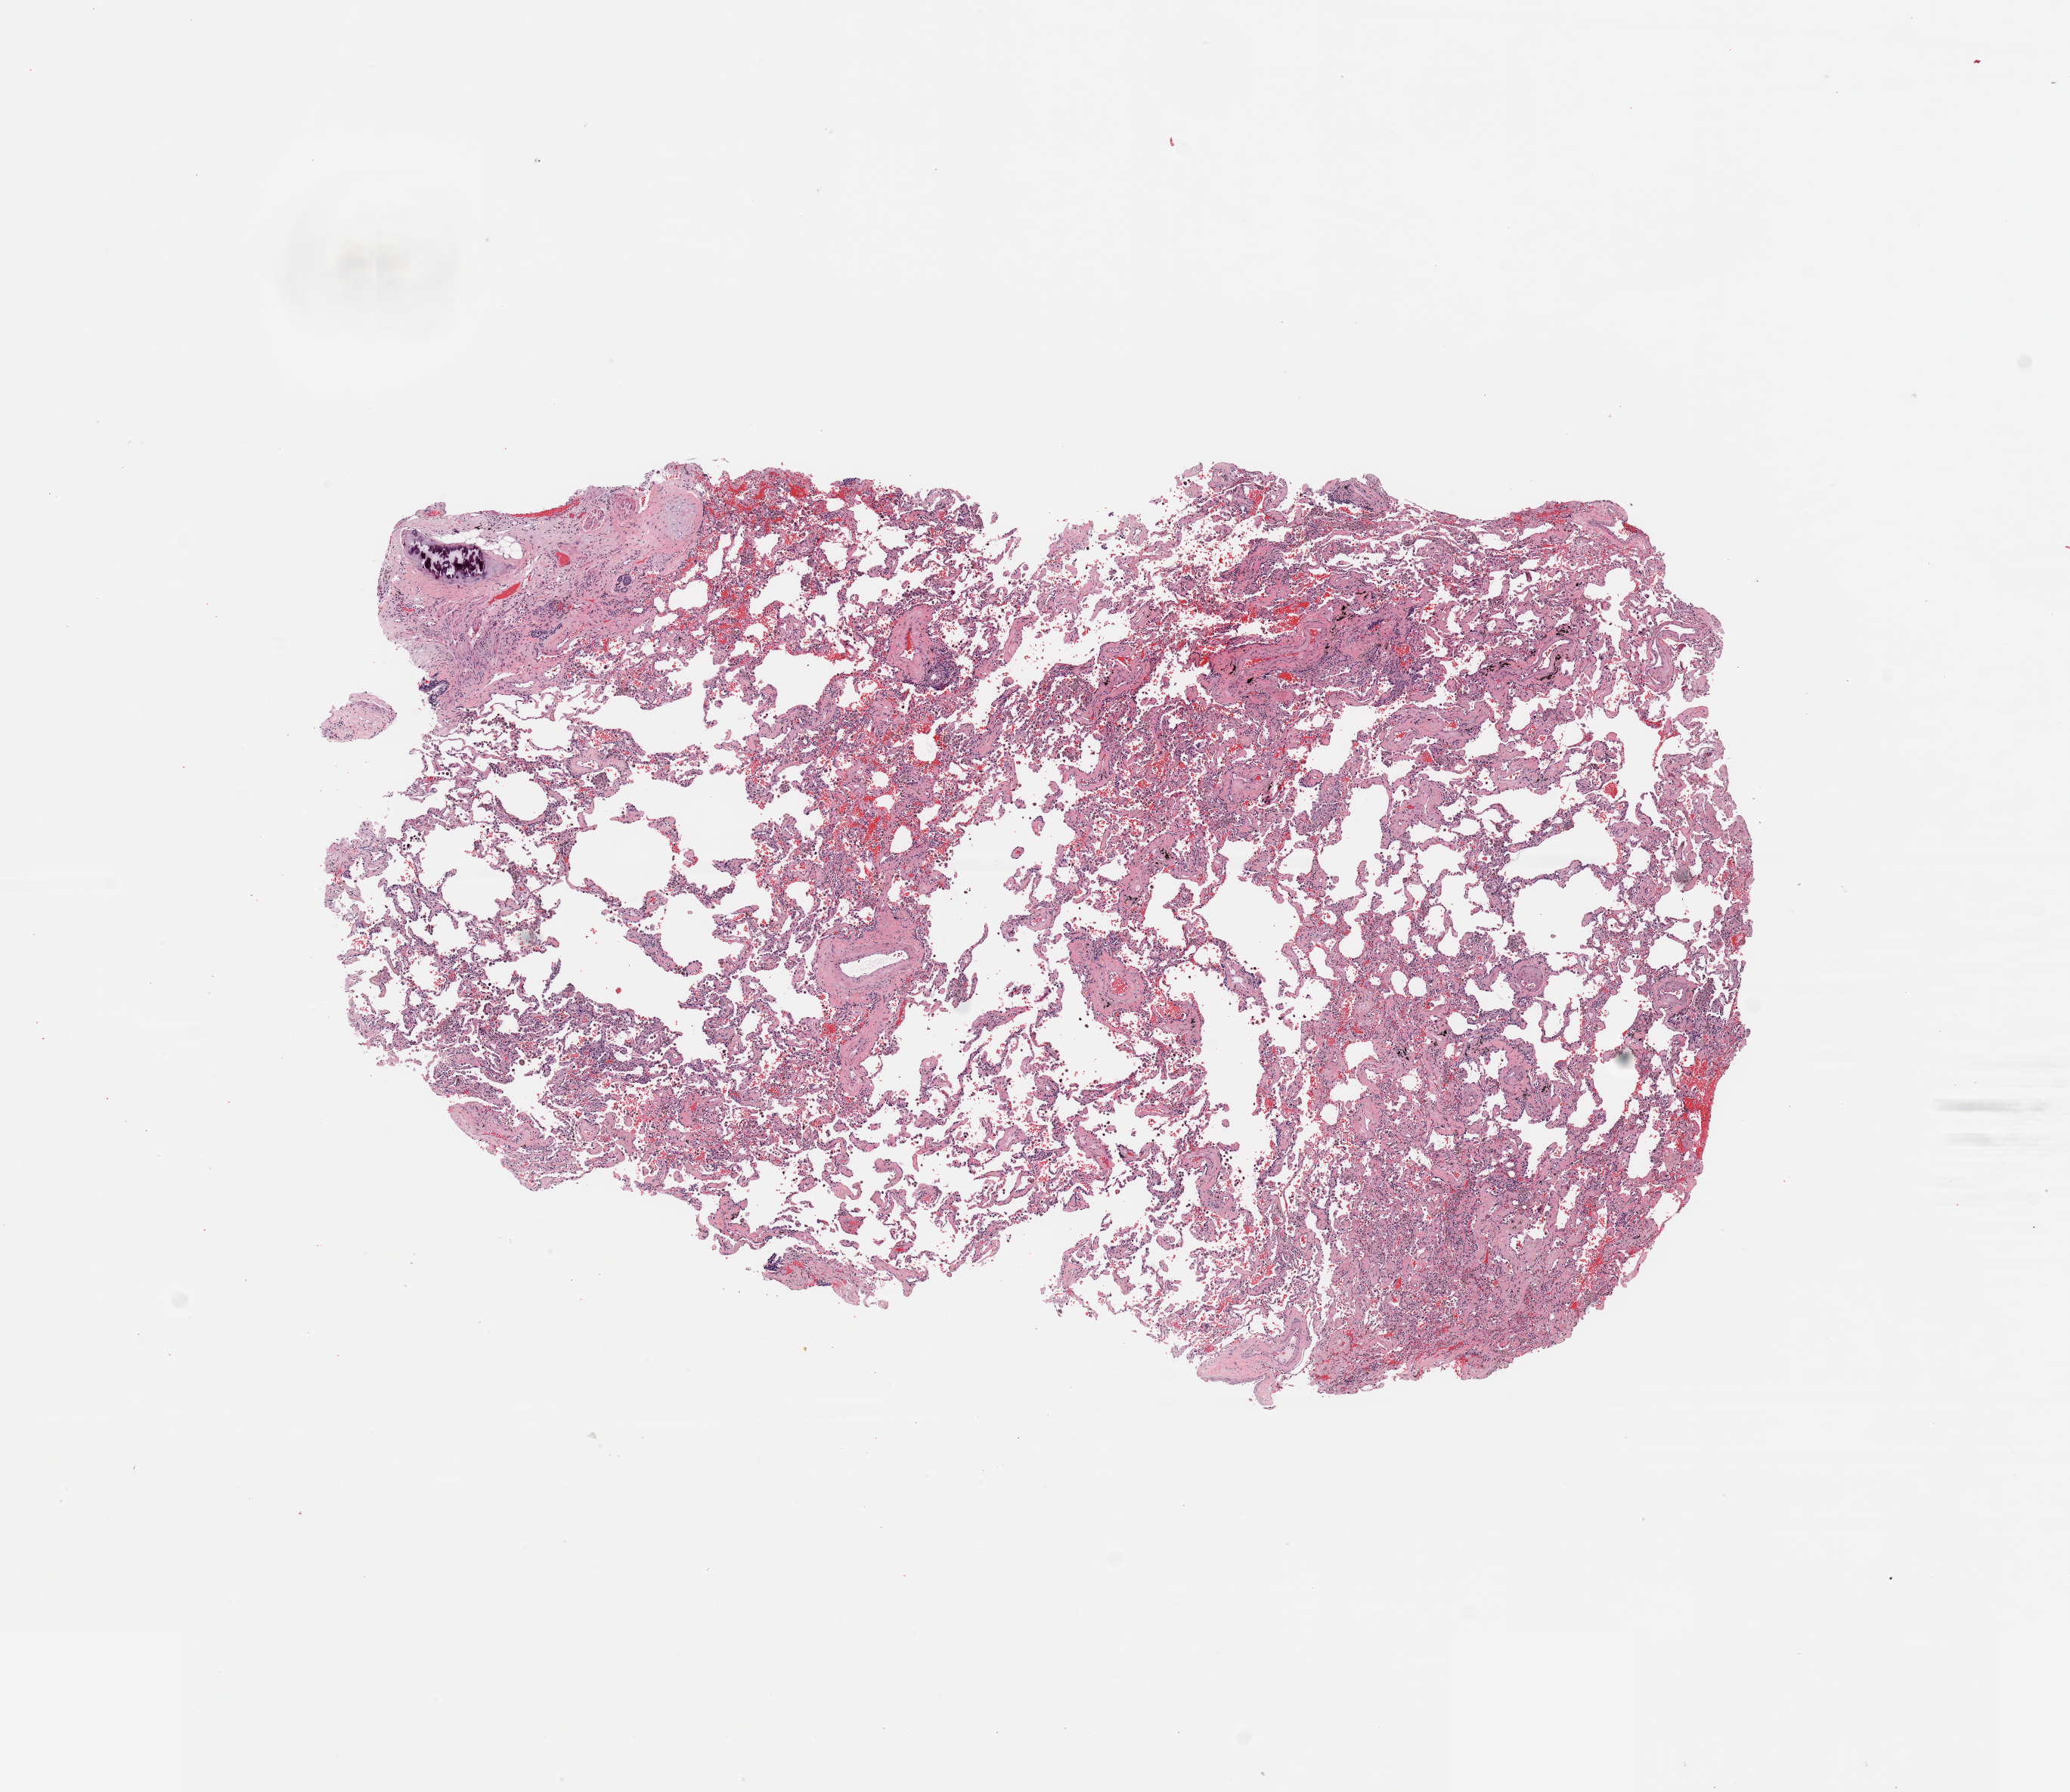
Whole-slide histology image, H&E — shown as a low-resolution overview of the whole scanned area (about 10.8 x 9.4 mm, from a 20x scan). Normal (non-tumour) tissue sample, sampled site: lung. 62-year-old female patient.
• this section: normal (non-tumour) tissue from the same patient
• patient diagnosis: Adenocarcinoma, NOS